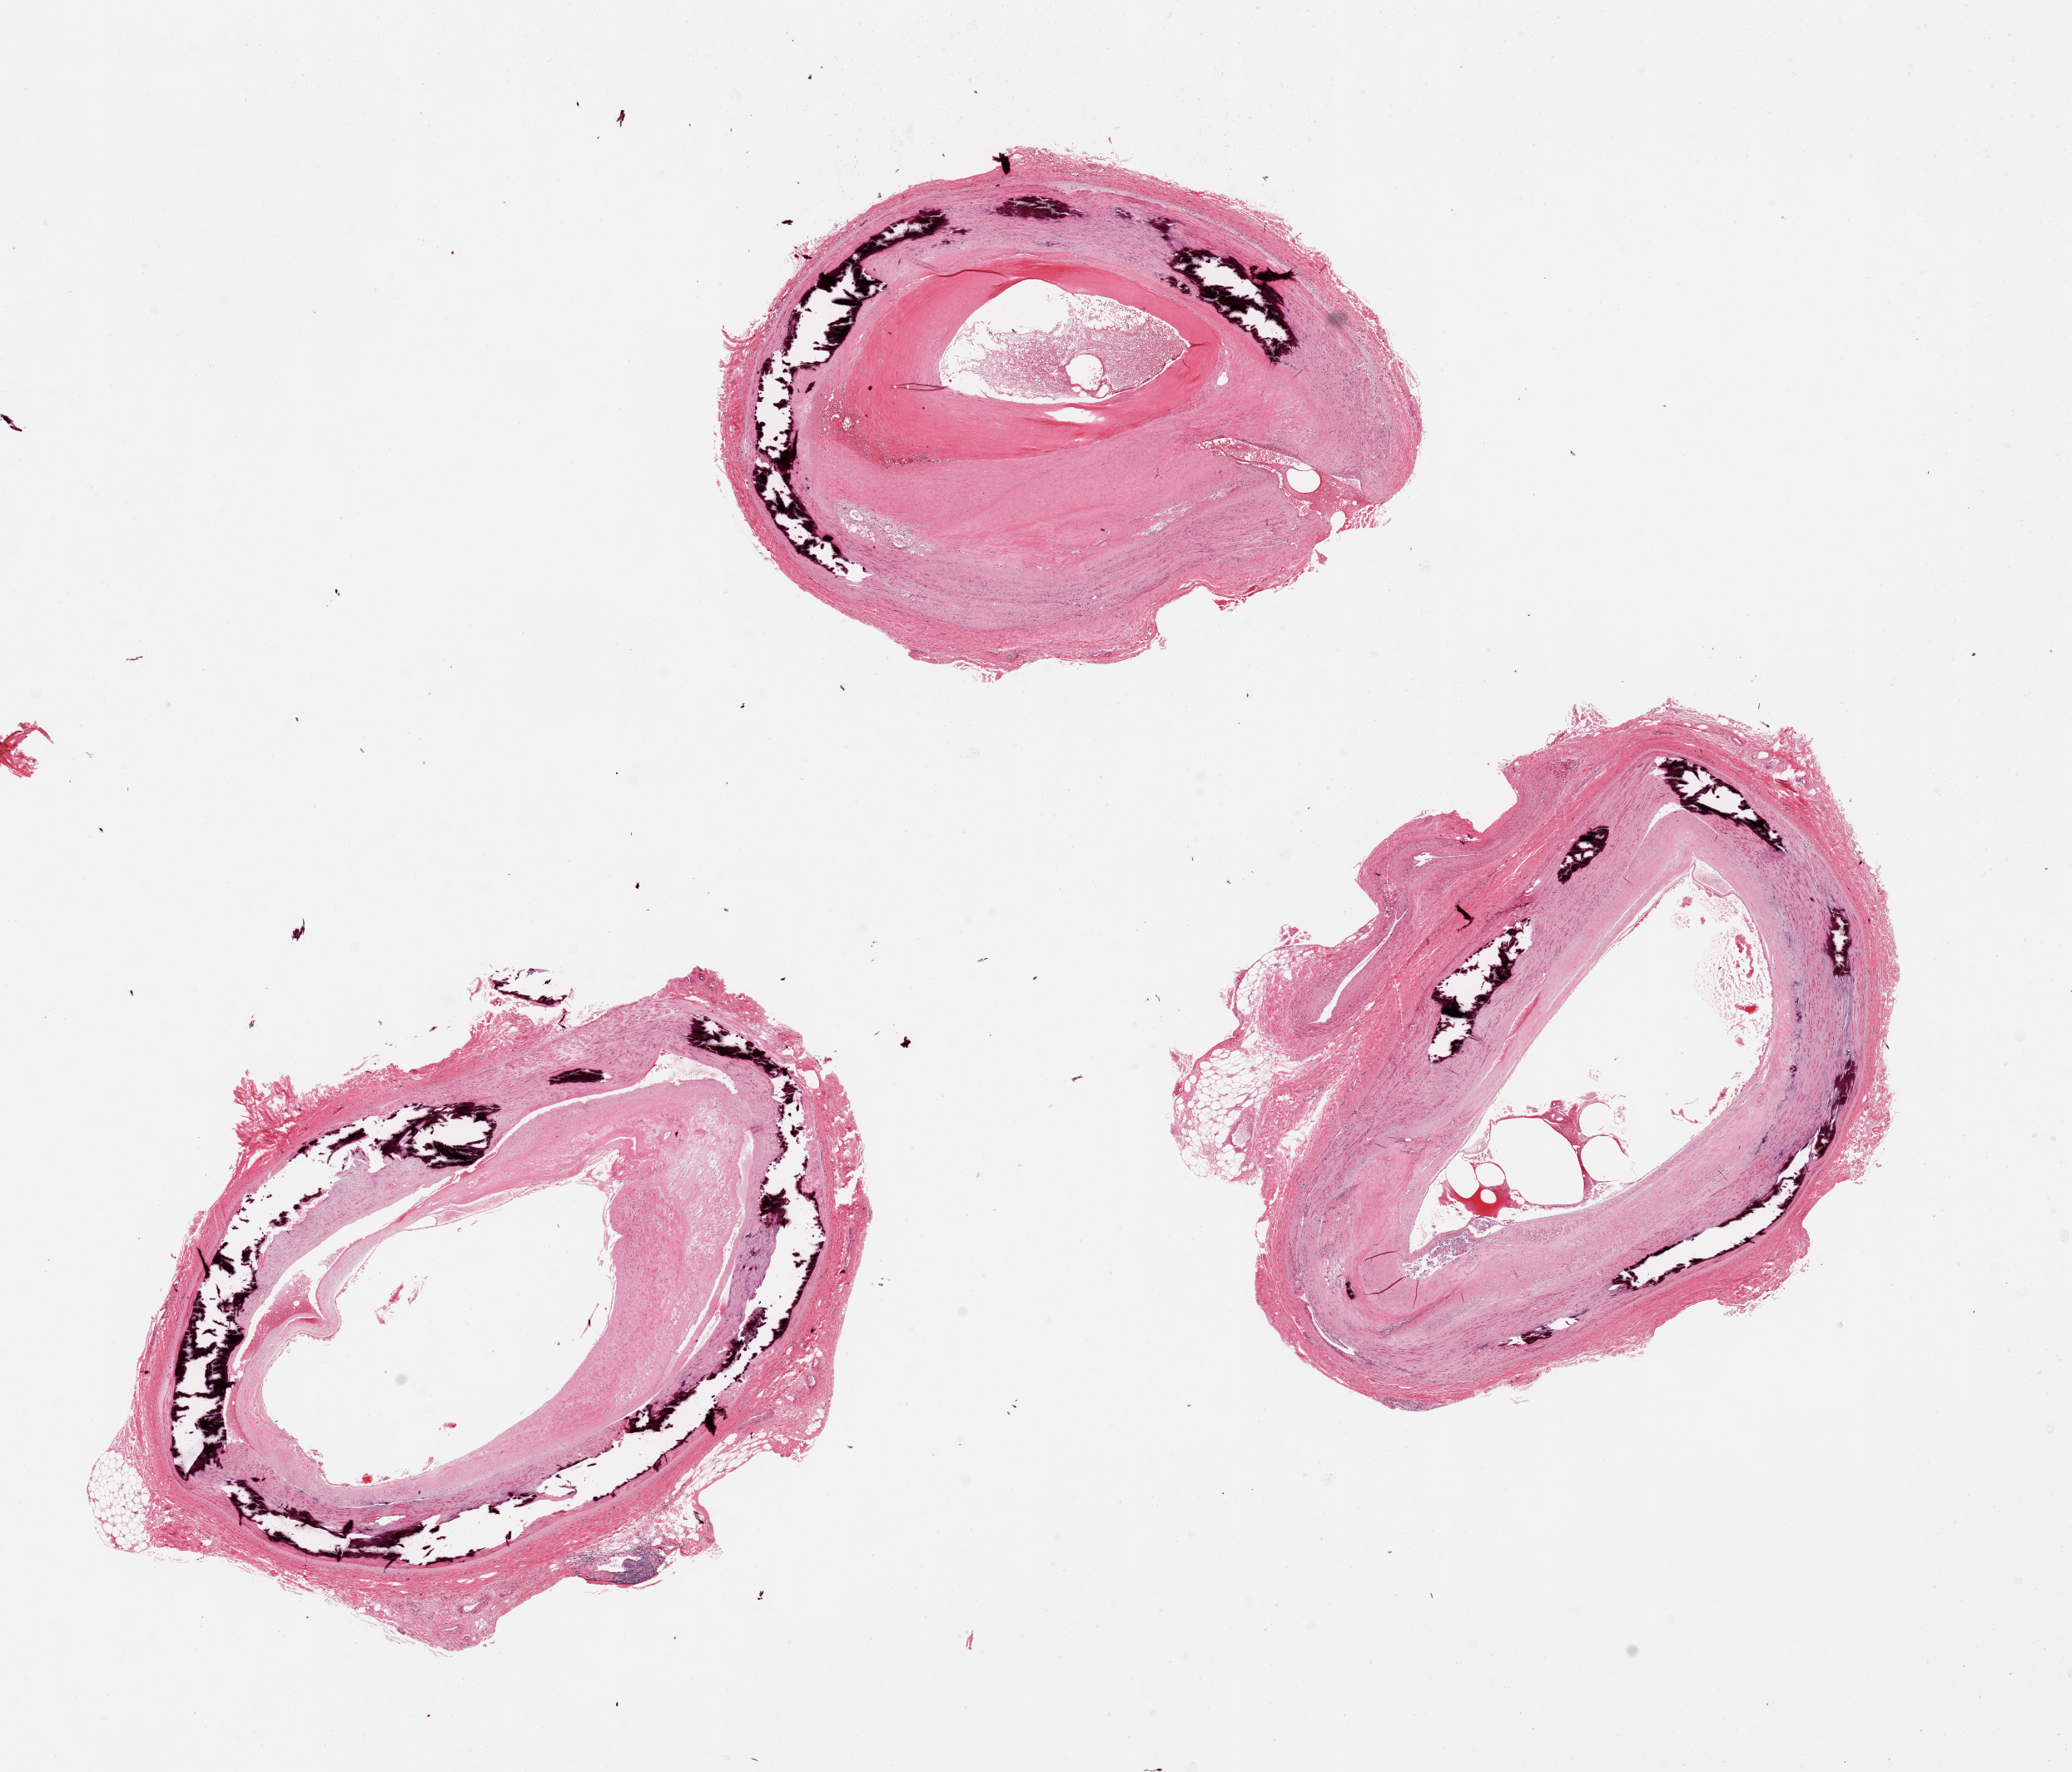
Digitized H&E-stained section, brightfield — whole scanned area (about 19.7 x 16.8 mm) shown as a low-resolution overview; PAXgene-fixed, paraffin-embedded tissue; sampled site (target tissue): tibial artery; donor tissue sample. Donor: female.
Reviewer comment on this tissue sample: 3 pieces ~6mm d. : well trimmed with only scant attached adipose tissue; atherosclerotic plaque with calcification and occlusion up to 70%.